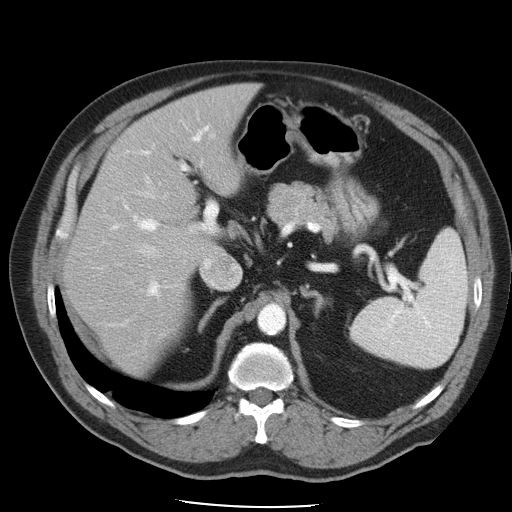
Contrast-enhanced abdominal CT, one axial slice. Position 32 of 49 along the scan axis. Reconstruction kernel STANDARD. Soft-tissue window (W 400 / L 40 HU). 512 × 512 image matrix, field of view 395 × 395 mm. Male patient, age 68 years. Case-level facts recorded for this patient, not image findings: diagnosis: colorectal cancer liver metastases, imaged before liver resection.
Structures marked on this image (manually delineated by an expert):
- hepatic veins: bounding box [x1, y1, x2, y2] px = [134, 175, 241, 287]
- liver: [67, 84, 255, 373]
- planned liver remnant (the part of the liver to remain after resection): [67, 84, 255, 373]
- portal vein (with intrahepatic branches): [101, 126, 215, 297]